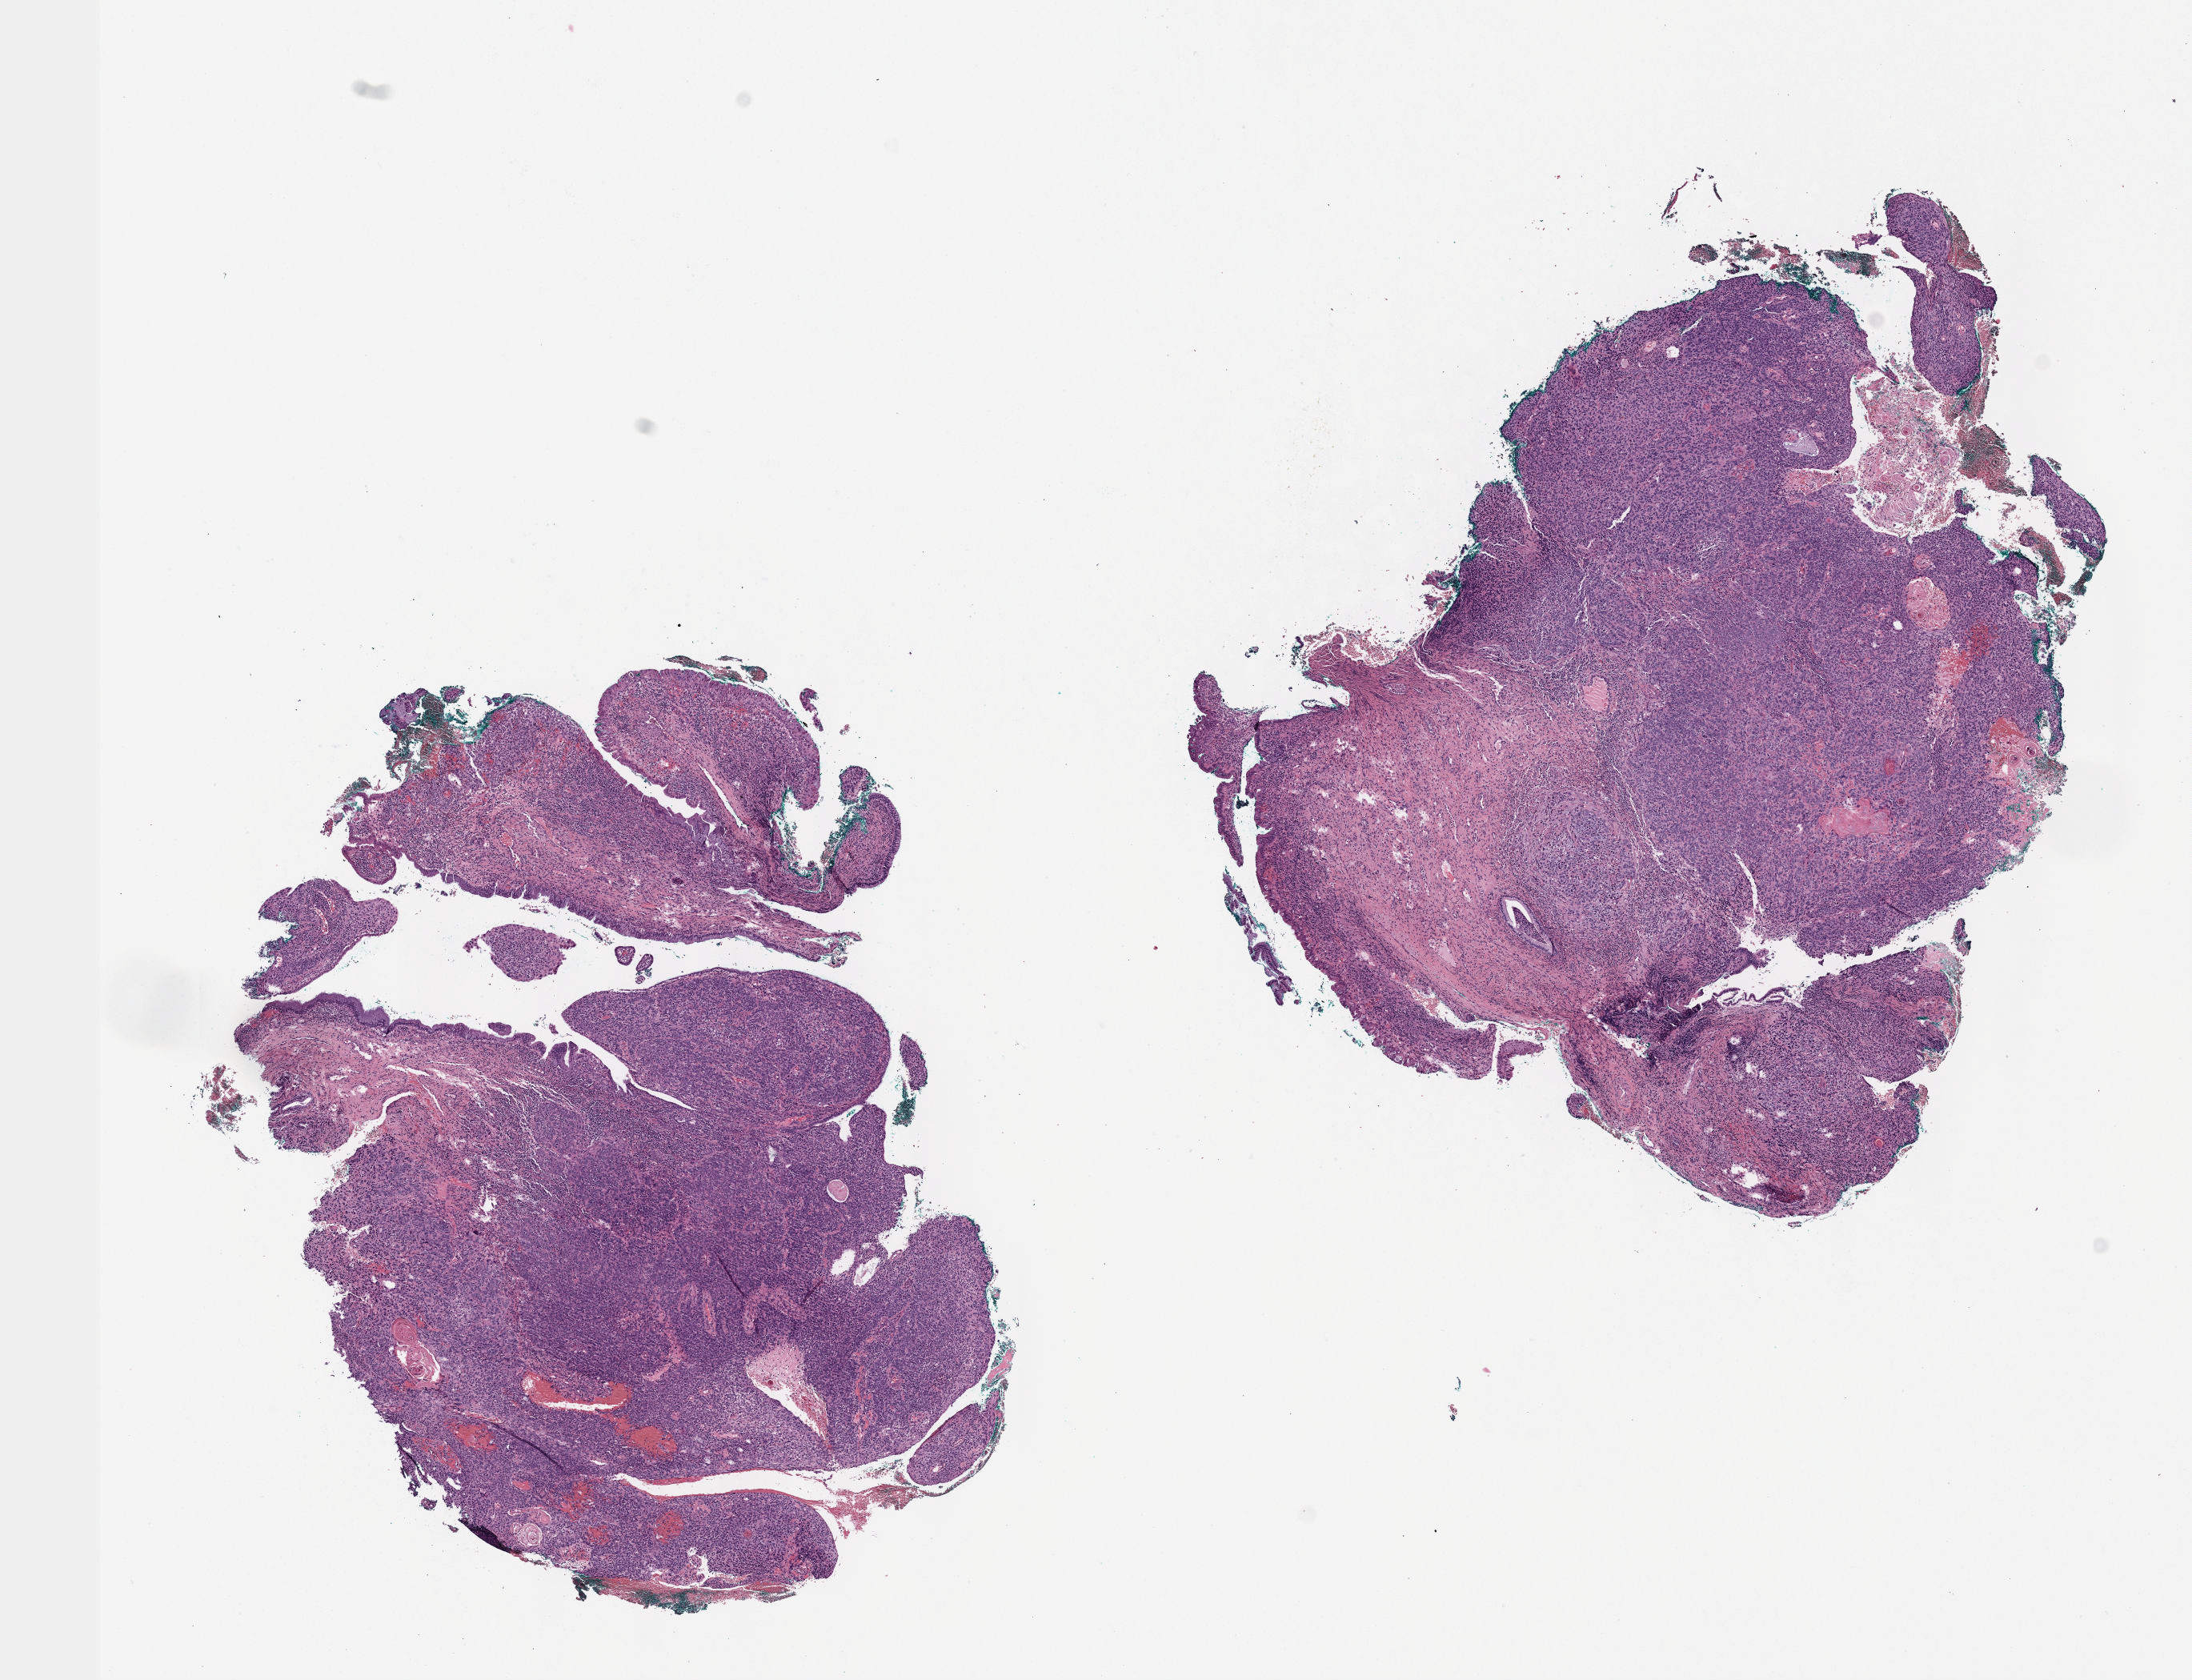
Digitized H&E-stained tissue section (whole slide) — a low-resolution overview of the entire scanned area, about 11.1 x 8.5 mm, FFPE section, sample: primary tumour, cervix. Female, age 39 years at initial diagnosis. Histologic grade: G2 (moderately differentiated).
Histologic diagnosis: Squamous cell carcinoma, NOS (cervix uteri). FIGO stage: IIB.